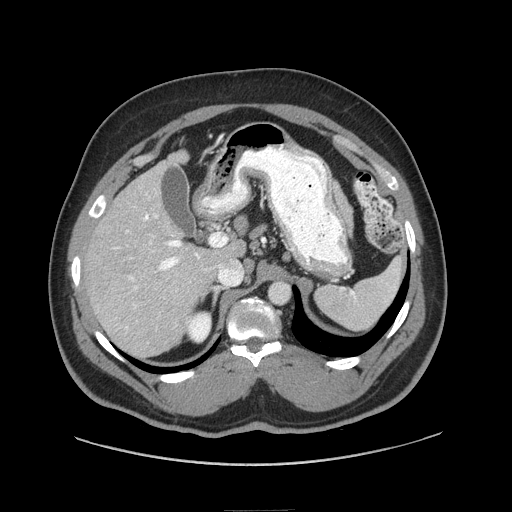
Contrast-enhanced abdominal CT (liver protocol), one axial slice; slice 48 of 87 in the series (ordered by position); reconstruction kernel STANDARD; soft-tissue window (W 400 / L 40 HU); 2.5 mm slice thickness; 512 × 512 image matrix, field of view 440 × 440 mm. Case-level facts recorded for this patient, not image findings: diagnosis: hepatocellular carcinoma (patient treated with transarterial chemoembolisation; whether this scan precedes or follows treatment is not stated here); TNM stage (as recorded): Stage-II; Child-Pugh class: A; tumour differentiation: moderately differentiated; tumour nodularity: uninodular.
Annotated regions visible in this slice (semi-automatic segmentation, software-assisted and operator-edited):
- liver parenchyma outside the tumour (the mass and vessels are separate outlines, so this box may not span the whole liver): bounding box (x1, y1, x2, y2) in pixels: (84, 150, 244, 356)
- liver vessels: (116, 193, 221, 329)